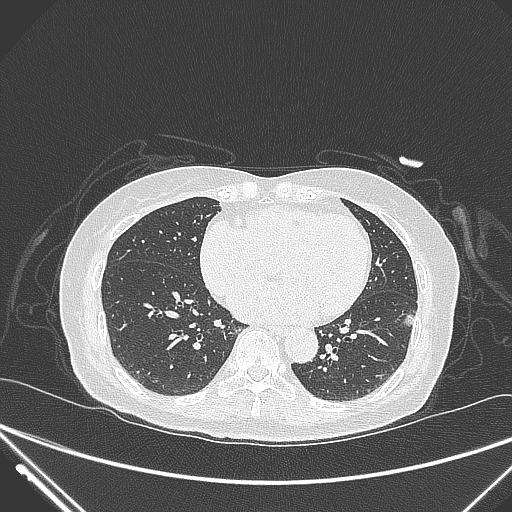
Chest CT, one axial slice; position 118 of 310 along the scan axis; lung window (W 1500 / L -600 HU); 1 mm slice thickness; 512 × 512 image matrix, field of view 377 × 377 mm. Patient: female, 82 years. From the clinical record (not read from this slice): clinical TNM (as recorded): T1c N0 M0; histopathological grade: G2.
Annotated regions visible in this slice (bounding box drawn by a radiologist):
- lung tumour (recorded histology: adenocarcinoma): bounding box (x1, y1, x2, y2) in pixels: (393, 308, 421, 340)